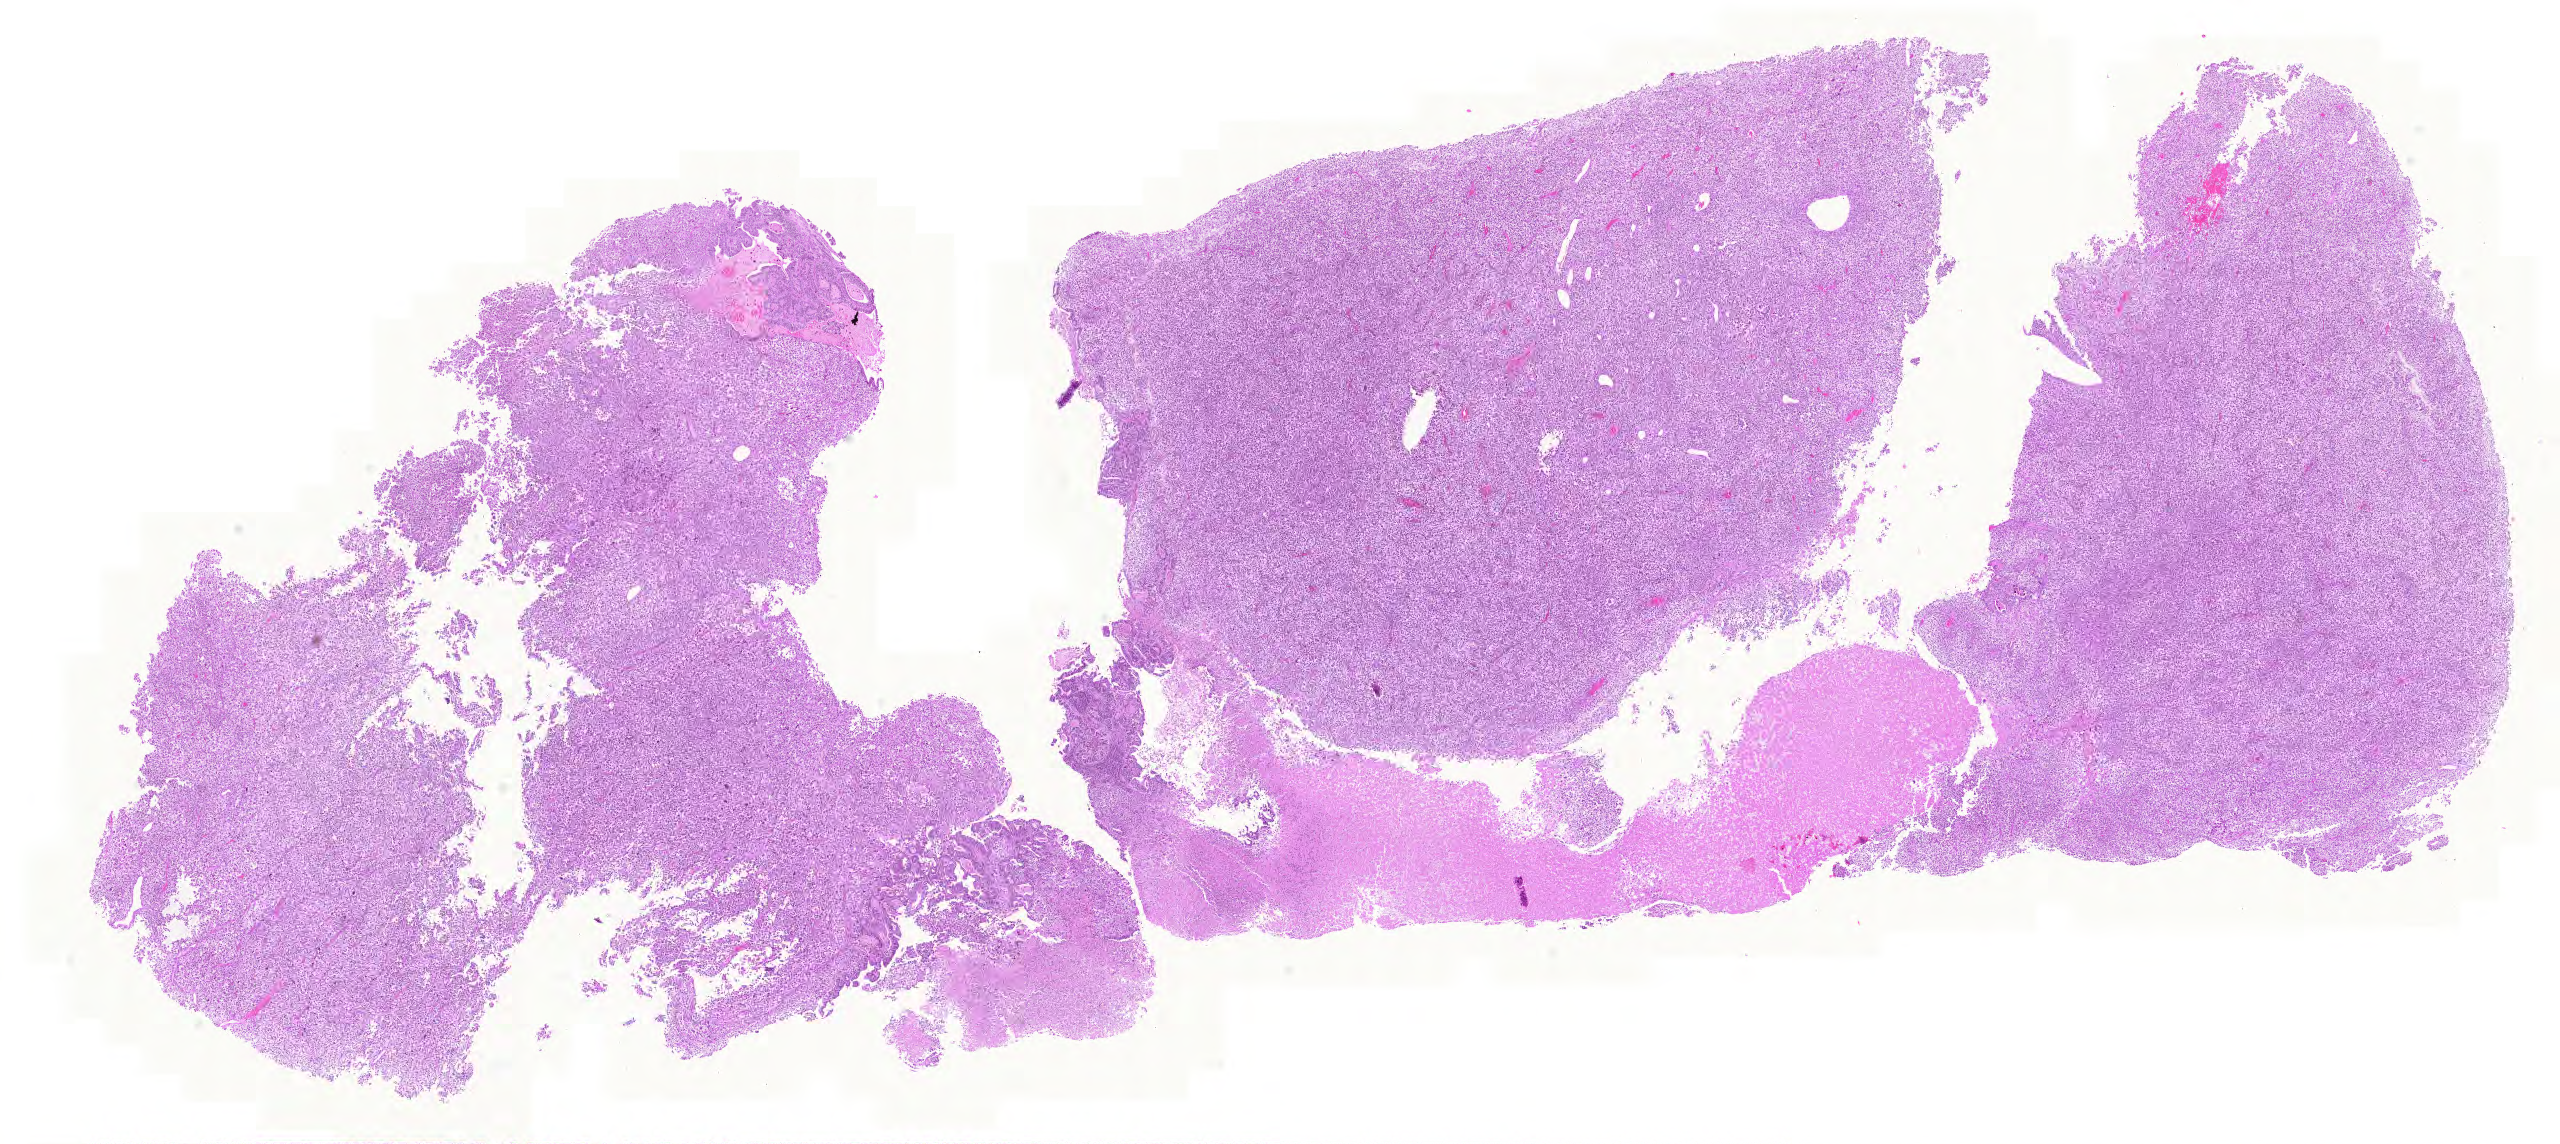
Hematoxylin and eosin (H&E) stained whole-slide image — low-resolution overview of the scanned area, about 19.0 x 8.5 mm (acquisition: 20x scan). FFPE section. Primary tumour sample from the lung. Male, age 65 years at initial diagnosis.
AJCC pathologic stage: IIB (5th edition). Pathologic diagnosis: Adenocarcinoma with mixed subtypes (middle lobe, lung). TNM: T2 N1 M0.